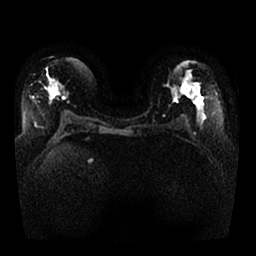
Breast MRI, one axial slice; slice 15 of 25 in the series (ordered by position); diffusion-weighted series; image 2 of 4 stored at this slice position (different b-values; order by instance number); 1.5 T; 256 × 256 image matrix. Female patient.
Annotated regions visible in this slice (outlined manually by an expert reader):
- tumour on diffusion-weighted imaging: bounding box (x1, y1, x2, y2) in pixels: (189, 86, 198, 94)